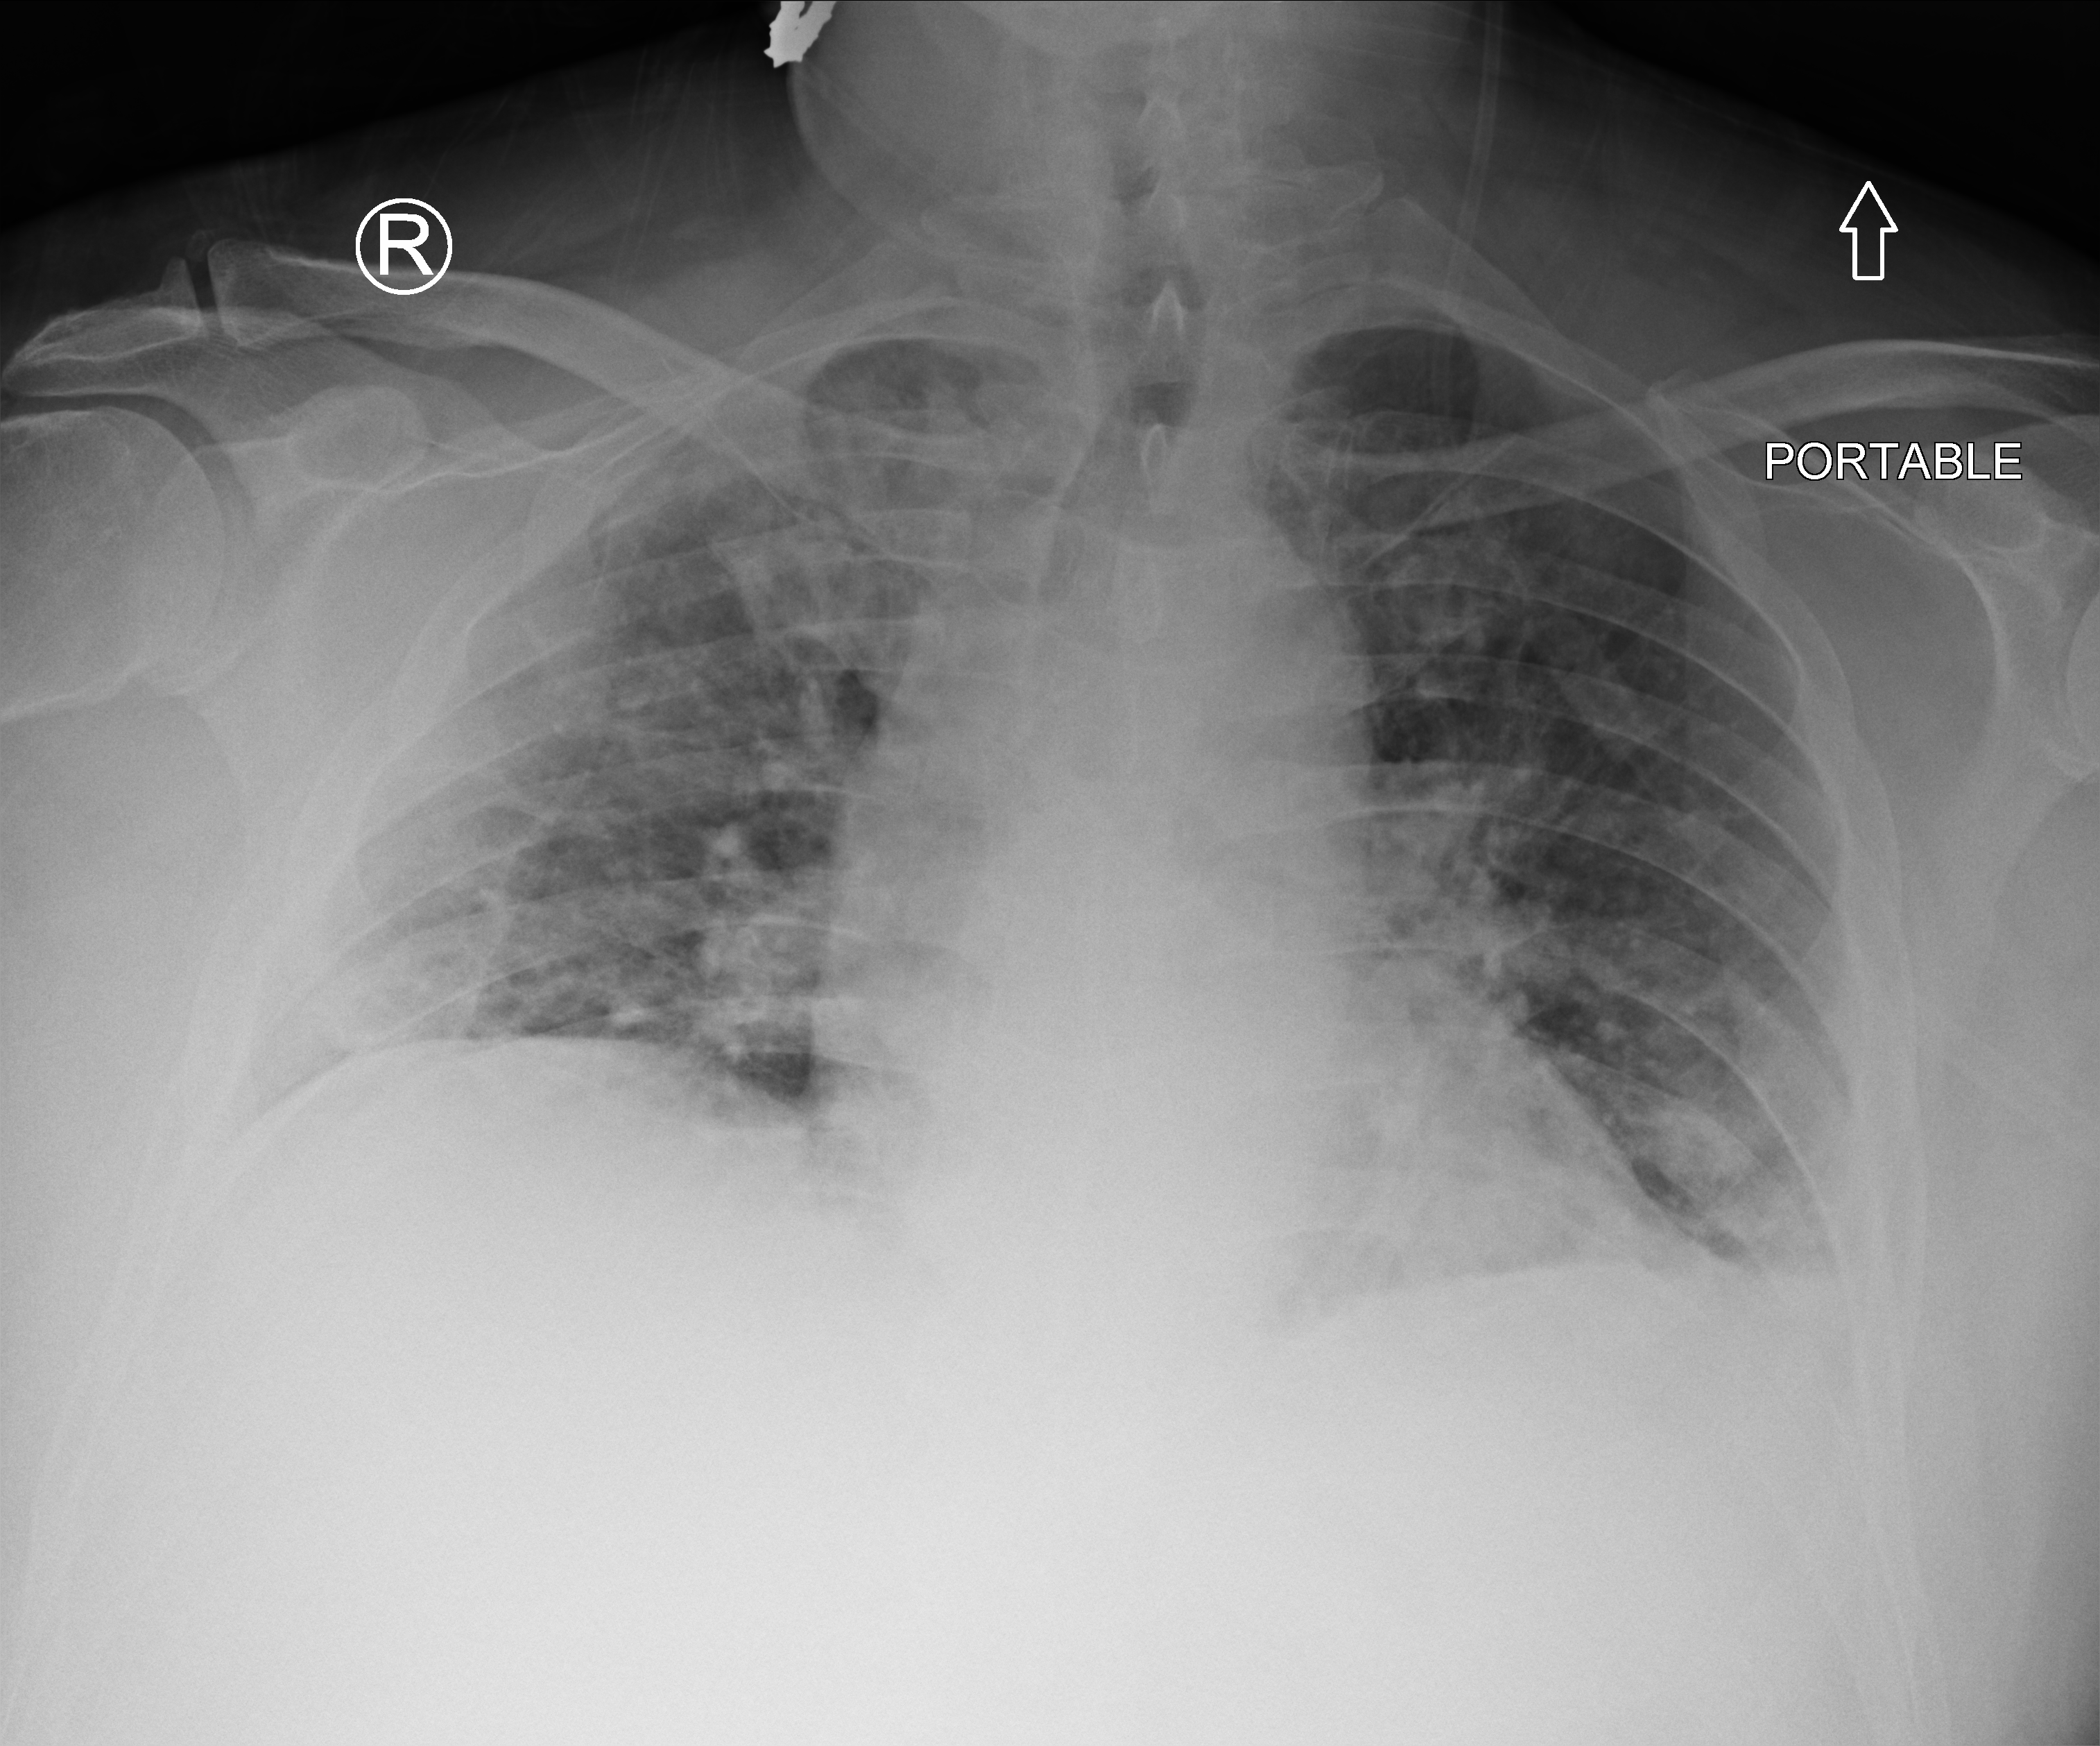
Bedside chest radiograph (computed radiography), anteroposterior (AP) projection. Male patient hospitalised with COVID-19, age 18–59 years.
Hospital-stay facts (about this admission, not read from this image; timing relative to this image not recorded): mechanically ventilated during this hospital stay: no; admitted to intensive care during this hospital stay: no.